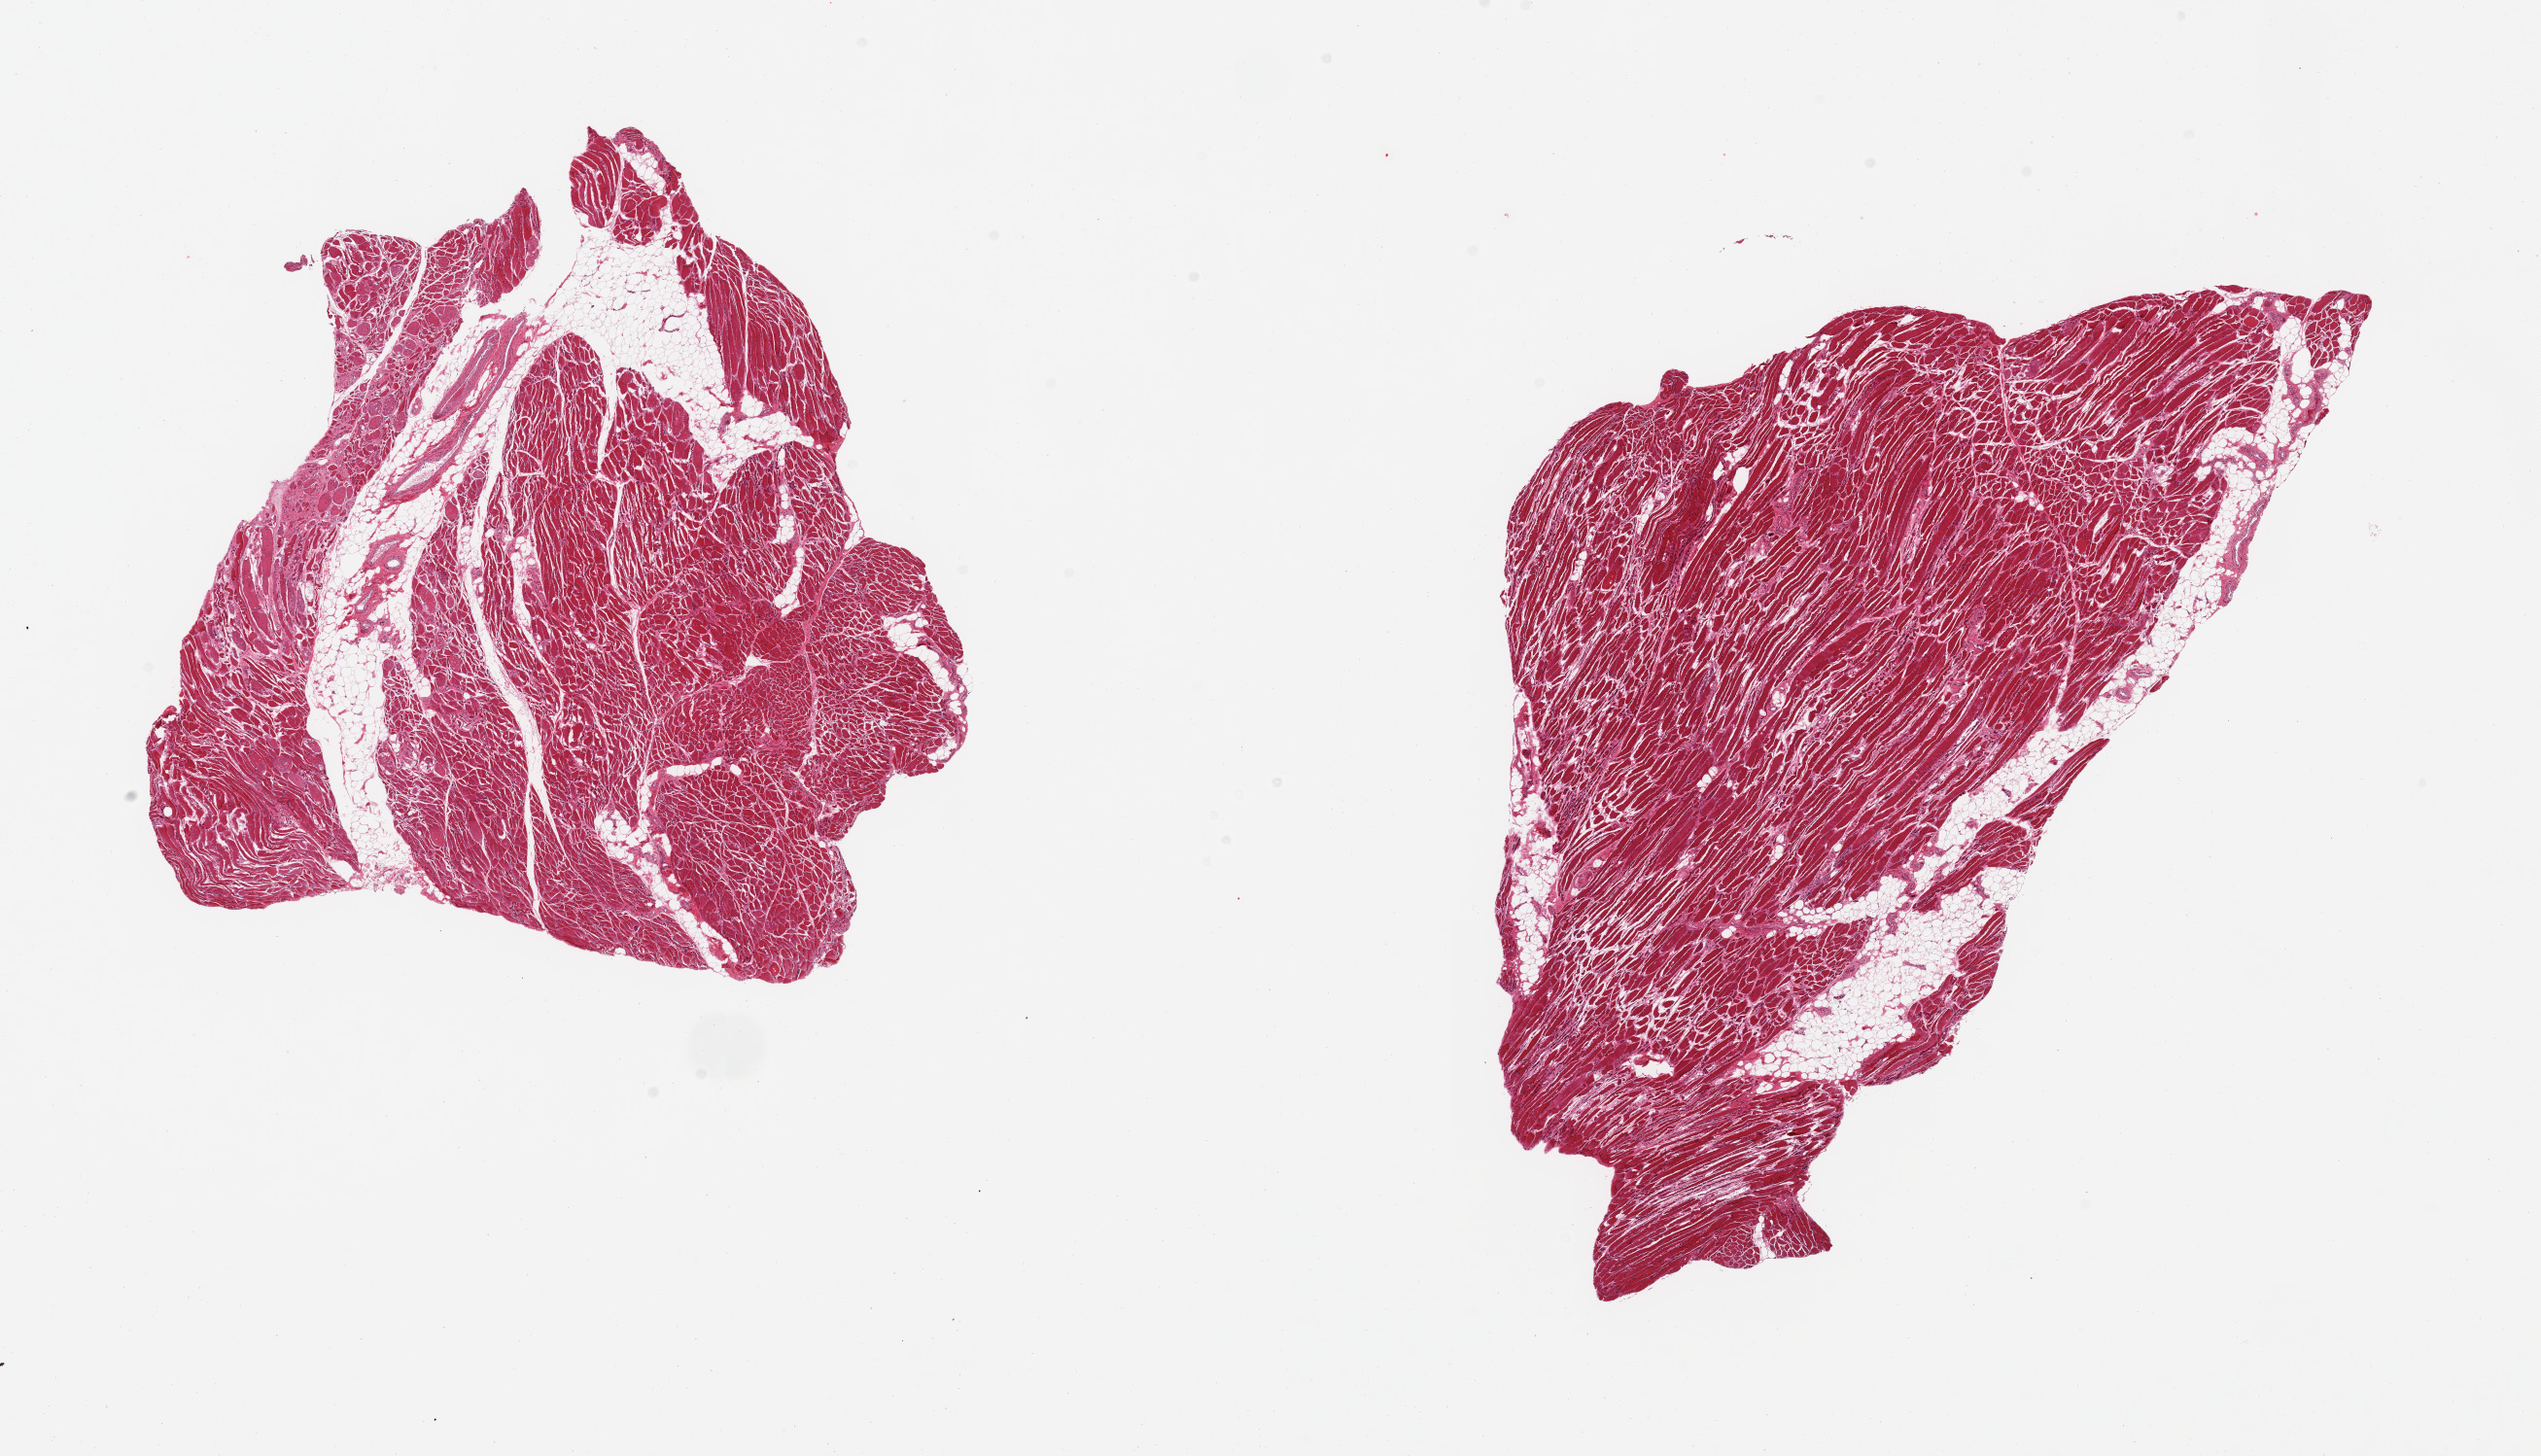
Whole-slide image, hematoxylin and eosin (H&E) stain — a low-resolution overview of the entire scanned area, about 20.7 x 11.8 mm (from a 20x scan); PAXgene-fixed, paraffin-embedded tissue; section of skeletal muscle (target tissue); donor tissue sample.
- reviewer comment on this tissue sample: 2 pieces; 10% internnal fat; focus of atrophy (2 sq mm)